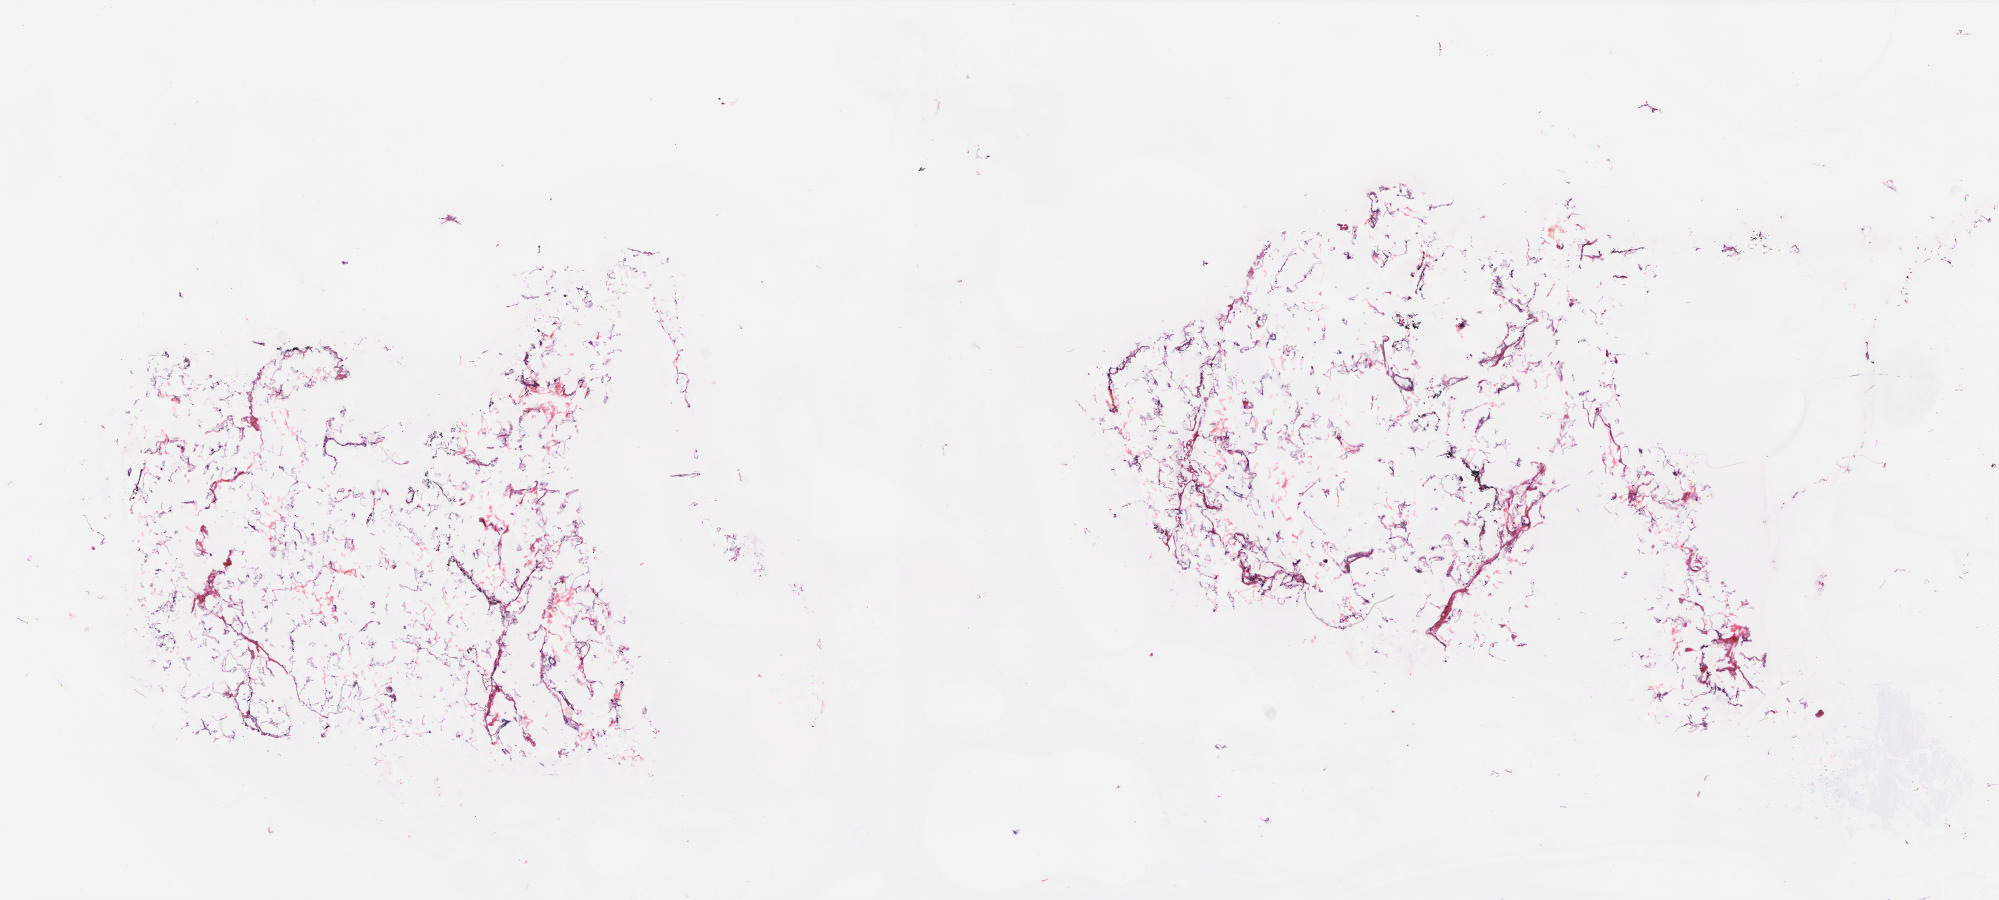
Digitized H&E-stained tissue section (whole slide), whole scanned area (about 16.0 x 7.2 mm, from a 20x scan) shown as a low-resolution overview. Frozen section from the top of the tissue portion. Solid tissue normal (non-tumour tissue) sample from the breast. Patient: female, age at initial diagnosis 45 years. Composition of this section per pathologist review: tumour cells 0%, tumour nuclei 0%, normal cells 0%, stromal cells 100%, necrosis 0%. Infiltration values recorded for this section: lymphocyte infiltration 0%, monocyte infiltration 0%, neutrophil infiltration 0%.
• this section: solid tissue normal sample (biorepository sample class)
• patient diagnosis: Lobular carcinoma, NOS